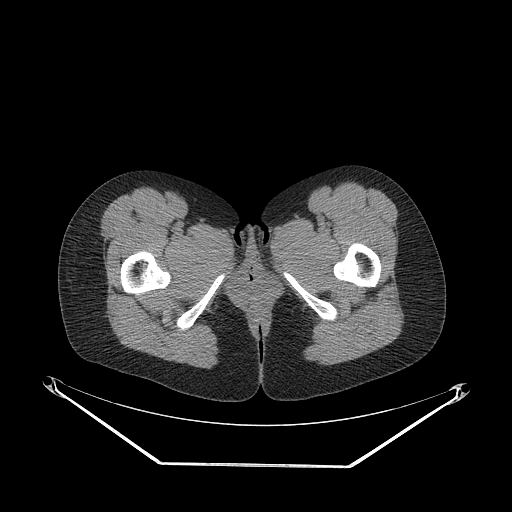
CT of an extremity soft-tissue mass (from a PET/CT study), one axial slice; slice 49 of 267 in the series (ordered by position); reconstruction kernel STANDARD; soft-tissue window (W 400 / L 40 HU); 3.75 mm slice thickness; 512 × 512 image matrix, field of view 500 × 500 mm. Female patient. Case-level facts recorded for this patient, not image findings: histological type: synovial sarcoma; grade: intermediate; site of the primary tumour: right thigh.
Structures marked on this image (expert contour drawn on MRI and transferred to this co-registered scan by the dataset authors):
- gross tumour volume including surrounding oedema: bounding box [x1, y1, x2, y2] px = [96, 224, 108, 238]
- gross tumour volume (mass): [96, 224, 108, 238]